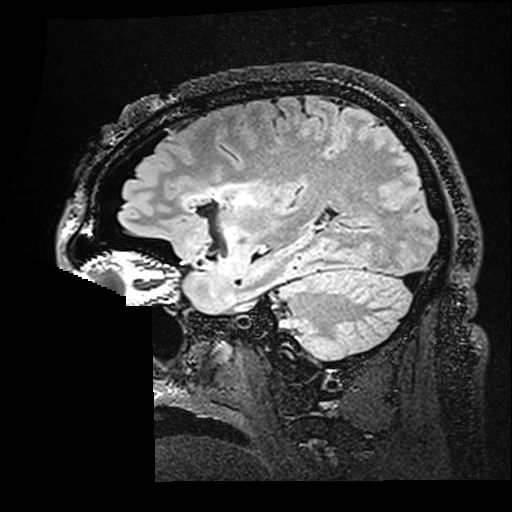
Brain MRI from a brain-tumour surgery series, one sagittal slice. Slice 118 of 176 in the series (ordered by position). T2 FLAIR. 1 mm slice thickness. 512 × 512 image matrix, field of view 250 × 250 mm. Case-level facts recorded for this patient, not image findings: histopathology: Astrocytoma; WHO grade: 2; IDH mutation: yes.
Outlined on this slice (manually delineated by an expert):
- residual tumour: bounding box (x1, y1, x2, y2) in pixels: (182, 184, 250, 236)